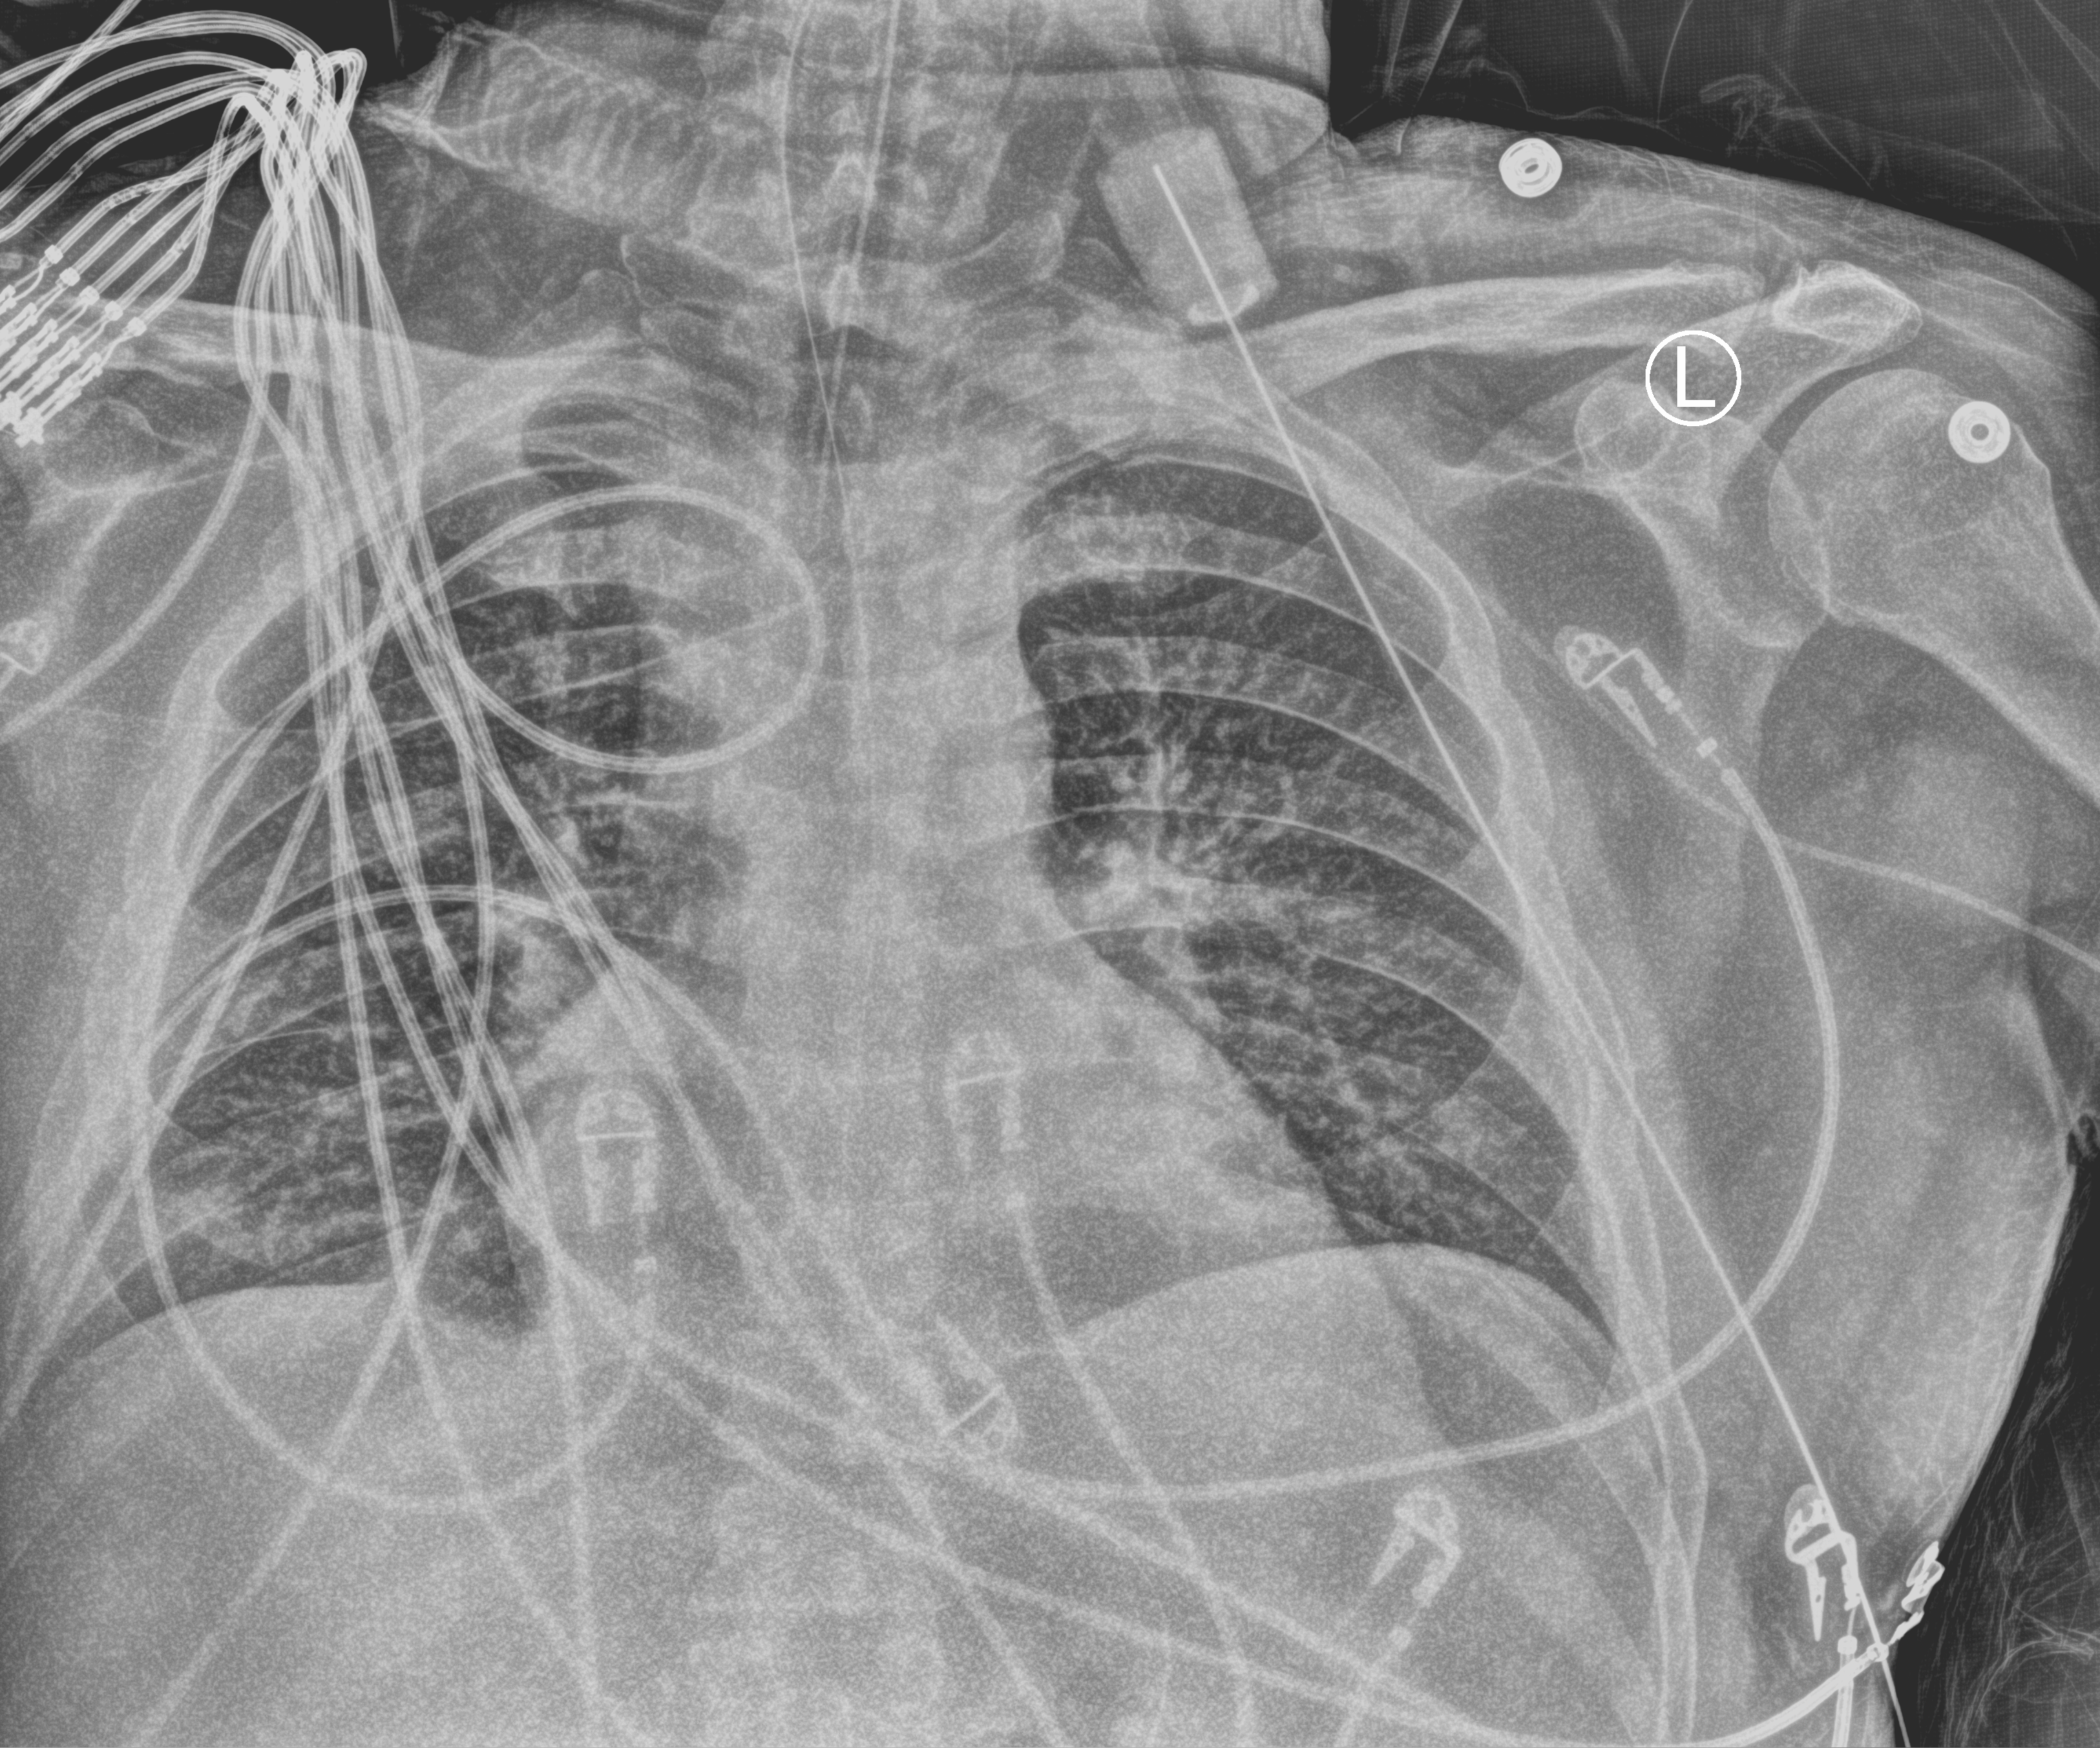
Portable chest radiograph. Patient hospitalised with COVID-19; male, aged 18–59 years.
Admission-level facts for this patient (not findings on this image; timing relative to this image not recorded): mechanically ventilated during this hospital stay: yes; admitted to intensive care during this hospital stay: yes.